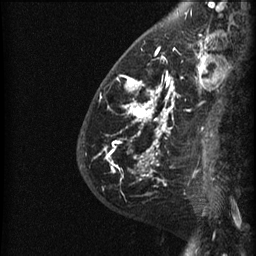
Breast MRI (dynamic contrast-enhanced), one sagittal slice; dynamic contrast-enhanced series, image 2 of 3 at this slice position (ordered by acquisition); 1.5 T; TE 4.2 ms, TR 22.7 ms; 1.5 mm slice thickness; 256 × 256 image matrix, field of view 180 × 180 mm. Patient: female, 48 years. Case-level facts recorded for this patient, not image findings: setting: breast cancer imaged before/during neoadjuvant chemotherapy; receptor status: triple-negative.
Structures marked on this image (semi-automatic segmentation, software-assisted and operator-edited):
- analysis volume of interest (the breast-tissue region the enhancement analysis was run in; not a lesion): bounding box <89,27,191,180> (left, top, right, bottom; pixels)
- tumour enhancement mask (voxels above the 90 % enhancement threshold inside the analysis volume of interest): <107,49,179,180>